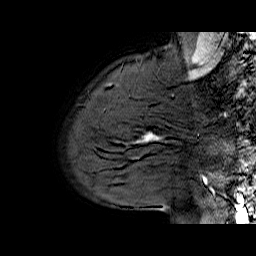
Breast MRI (dynamic contrast-enhanced), one sagittal slice; position 53 of 70 along the scan axis; dynamic contrast-enhanced series, time point 2 of 6 at this slice position (early post-contrast); 1.5 T; TE 6.5 ms, TR 33 ms; 4 mm slice thickness; 256 × 256 image matrix, field of view 200 × 200 mm. Female patient. From the clinical record (not read from this slice): setting: breast cancer imaged before/during neoadjuvant chemotherapy; receptor status: HER2-positive.
Annotated regions visible in this slice (semi-automatic segmentation, software-assisted and operator-edited):
- analysis volume of interest (the breast-tissue region the enhancement analysis was run in; not a lesion): bounding box [x1, y1, x2, y2] px = [113, 112, 174, 170]
- tumour enhancement mask (voxels above the 100 % enhancement threshold inside the analysis volume of interest): [139, 132, 154, 141]